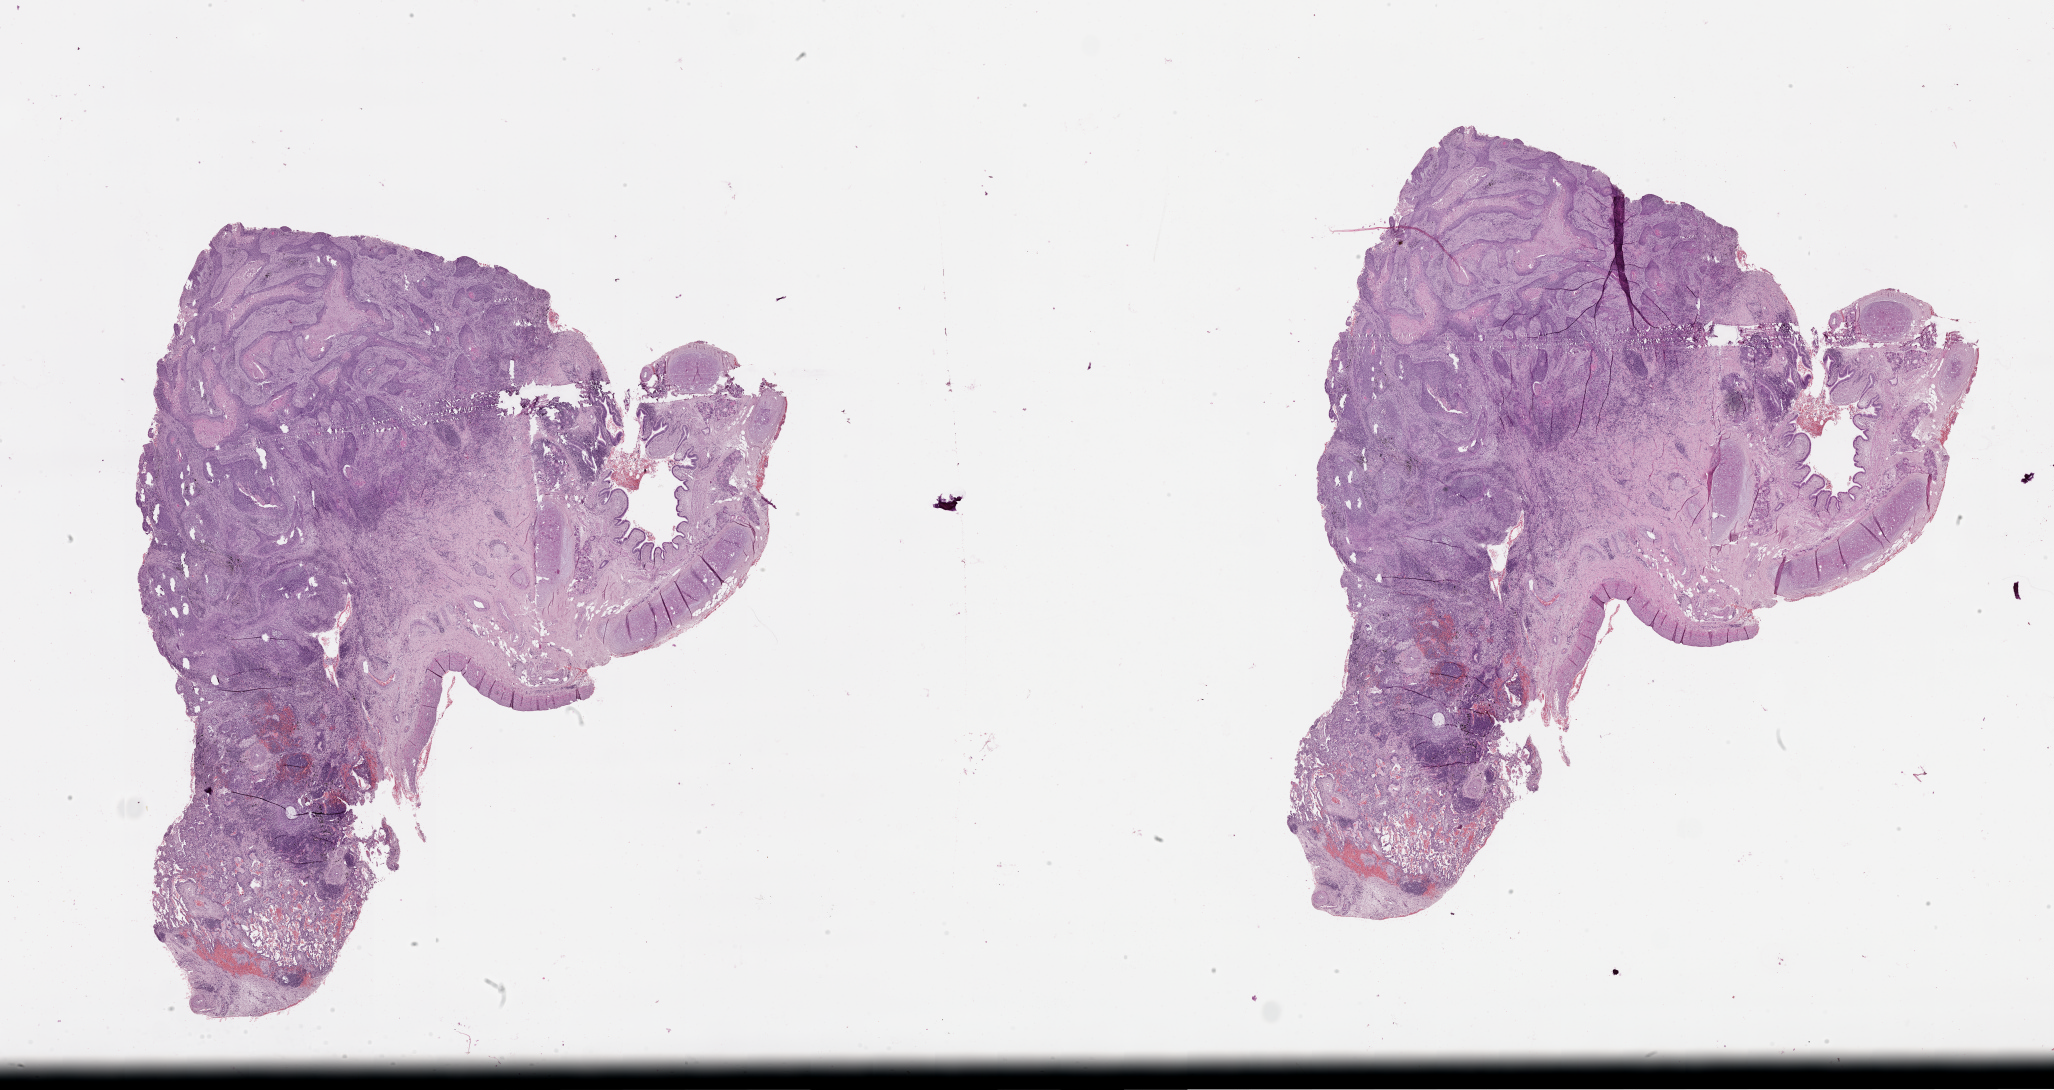
Whole-slide histology image, Hematoxylin and eosin (H&E) stained, shown as a low-resolution overview of the whole scanned area (about 33.1 x 17.6 mm); lung, tumour tissue. Female, 63 y/o.
Patient diagnosis (cohort enrolment): squamous cell carcinoma (lung).